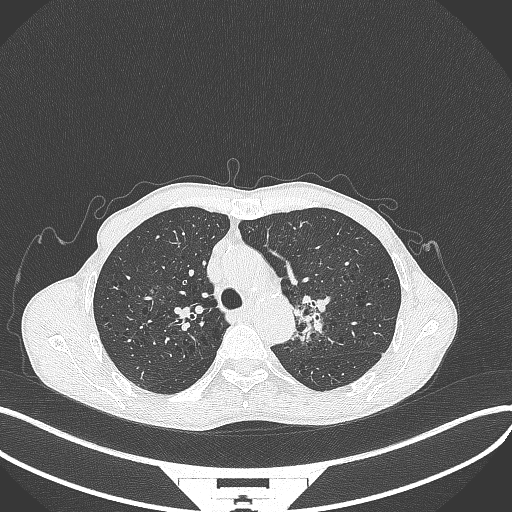
Chest CT, one axial slice. Reconstruction kernel B70f. 120 kVp. Lung window (W 1500 / L -600 HU). 1 mm slice thickness. 512 × 512 image matrix, field of view 400 × 400 mm. Male patient, age 65 years. Case-level facts recorded for this patient, not image findings: clinical TNM (as recorded): T2b N0 M0; histopathological grade: G2.
Annotated regions visible in this slice (bounding box drawn by a radiologist):
- lung tumour (recorded histology: adenocarcinoma): bounding box (x1, y1, x2, y2) in pixels: (291, 286, 339, 348)